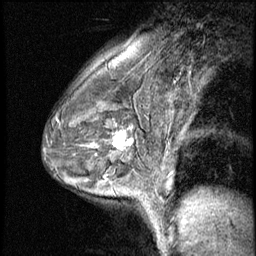
Breast MRI (dynamic contrast-enhanced), one sagittal slice. Position 40 of 56 along the scan axis. 3 images stored at this slice position (order not interpretable as contrast timing). 1.5 T. TE 4.2 ms, TR 8.7 ms. 2.5 mm slice thickness. 256 × 256 image matrix, field of view 180 × 180 mm. Female patient, age 43 years. From the clinical record (not read from this slice): setting: breast cancer imaged before/during neoadjuvant chemotherapy; receptor status: HR-positive, HER2-negative.
Structures marked on this image (semi-automatic segmentation, software-assisted and operator-edited):
- analysis volume of interest (the breast-tissue region the enhancement analysis was run in; not a lesion): bounding box [x1, y1, x2, y2] px = [101, 120, 145, 165]
- tumour enhancement mask (voxels above the 140 % enhancement threshold inside the analysis volume of interest): [113, 131, 133, 149]